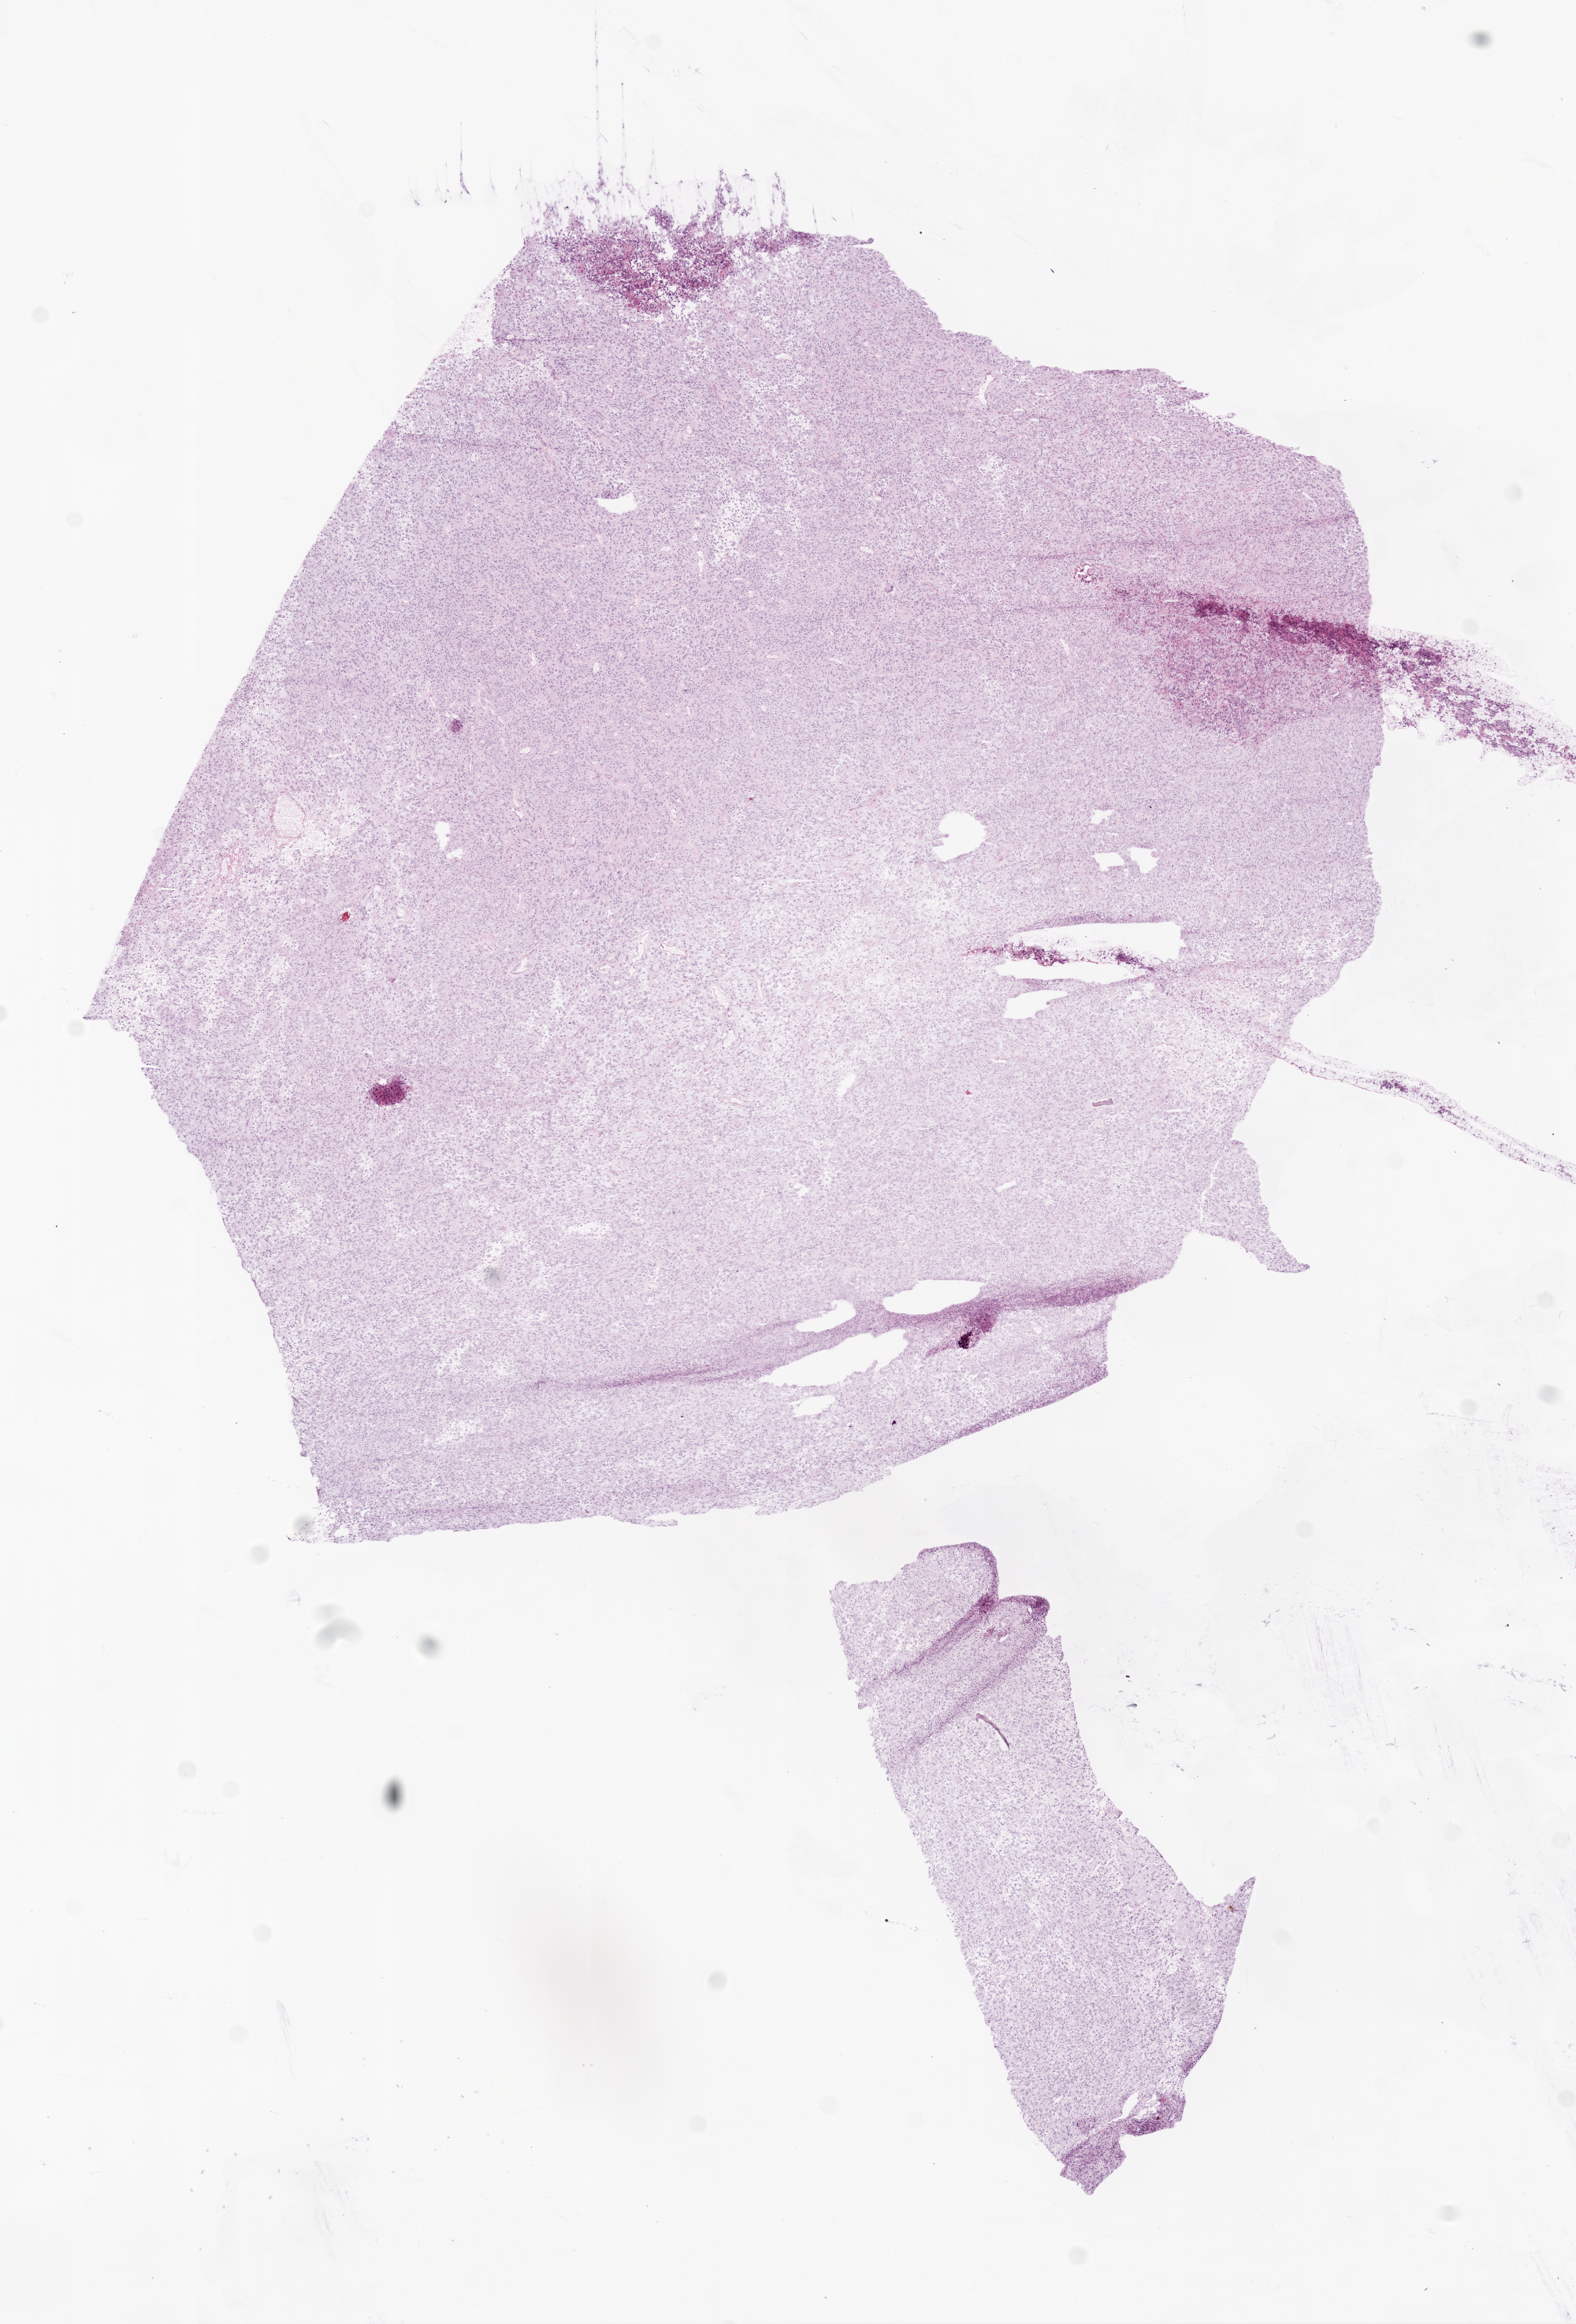
H&E-stained whole-slide image — whole scanned area (about 8.0 x 11.8 mm, from a 20x scan) shown as a low-resolution overview; frozen section from the top of the tissue portion; brain, primary tumour sample. Patient: female, age at initial diagnosis 49 years. Slide review estimates, as recorded: tumour cells 95%, tumour nuclei 95%, normal cells 0%, stromal cells 0%, necrosis 5%.
- diagnosis: Glioblastoma